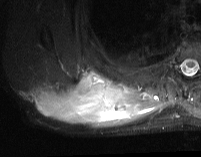
MRI of an extremity soft-tissue mass, one axial slice. Position 23 of 74 along the scan axis. STIR. MR volume resampled by the dataset authors to the PET/CT grid (not the native acquisition matrix). 3.27 mm slice thickness. 201 × 157 image matrix. Male patient. From the clinical record (not read from this slice): histological type: pleiomorphic spindle cell undifferentiated; grade: high; site of the primary tumour: right parascapusular.
Structures marked on this image (expert contour drawn on MRI and transferred to this co-registered scan by the dataset authors):
- gross tumour volume including surrounding oedema: box from (x=28, y=70) to (x=164, y=129) px
- gross tumour volume (mass): (x=35, y=73)–(x=130, y=124)